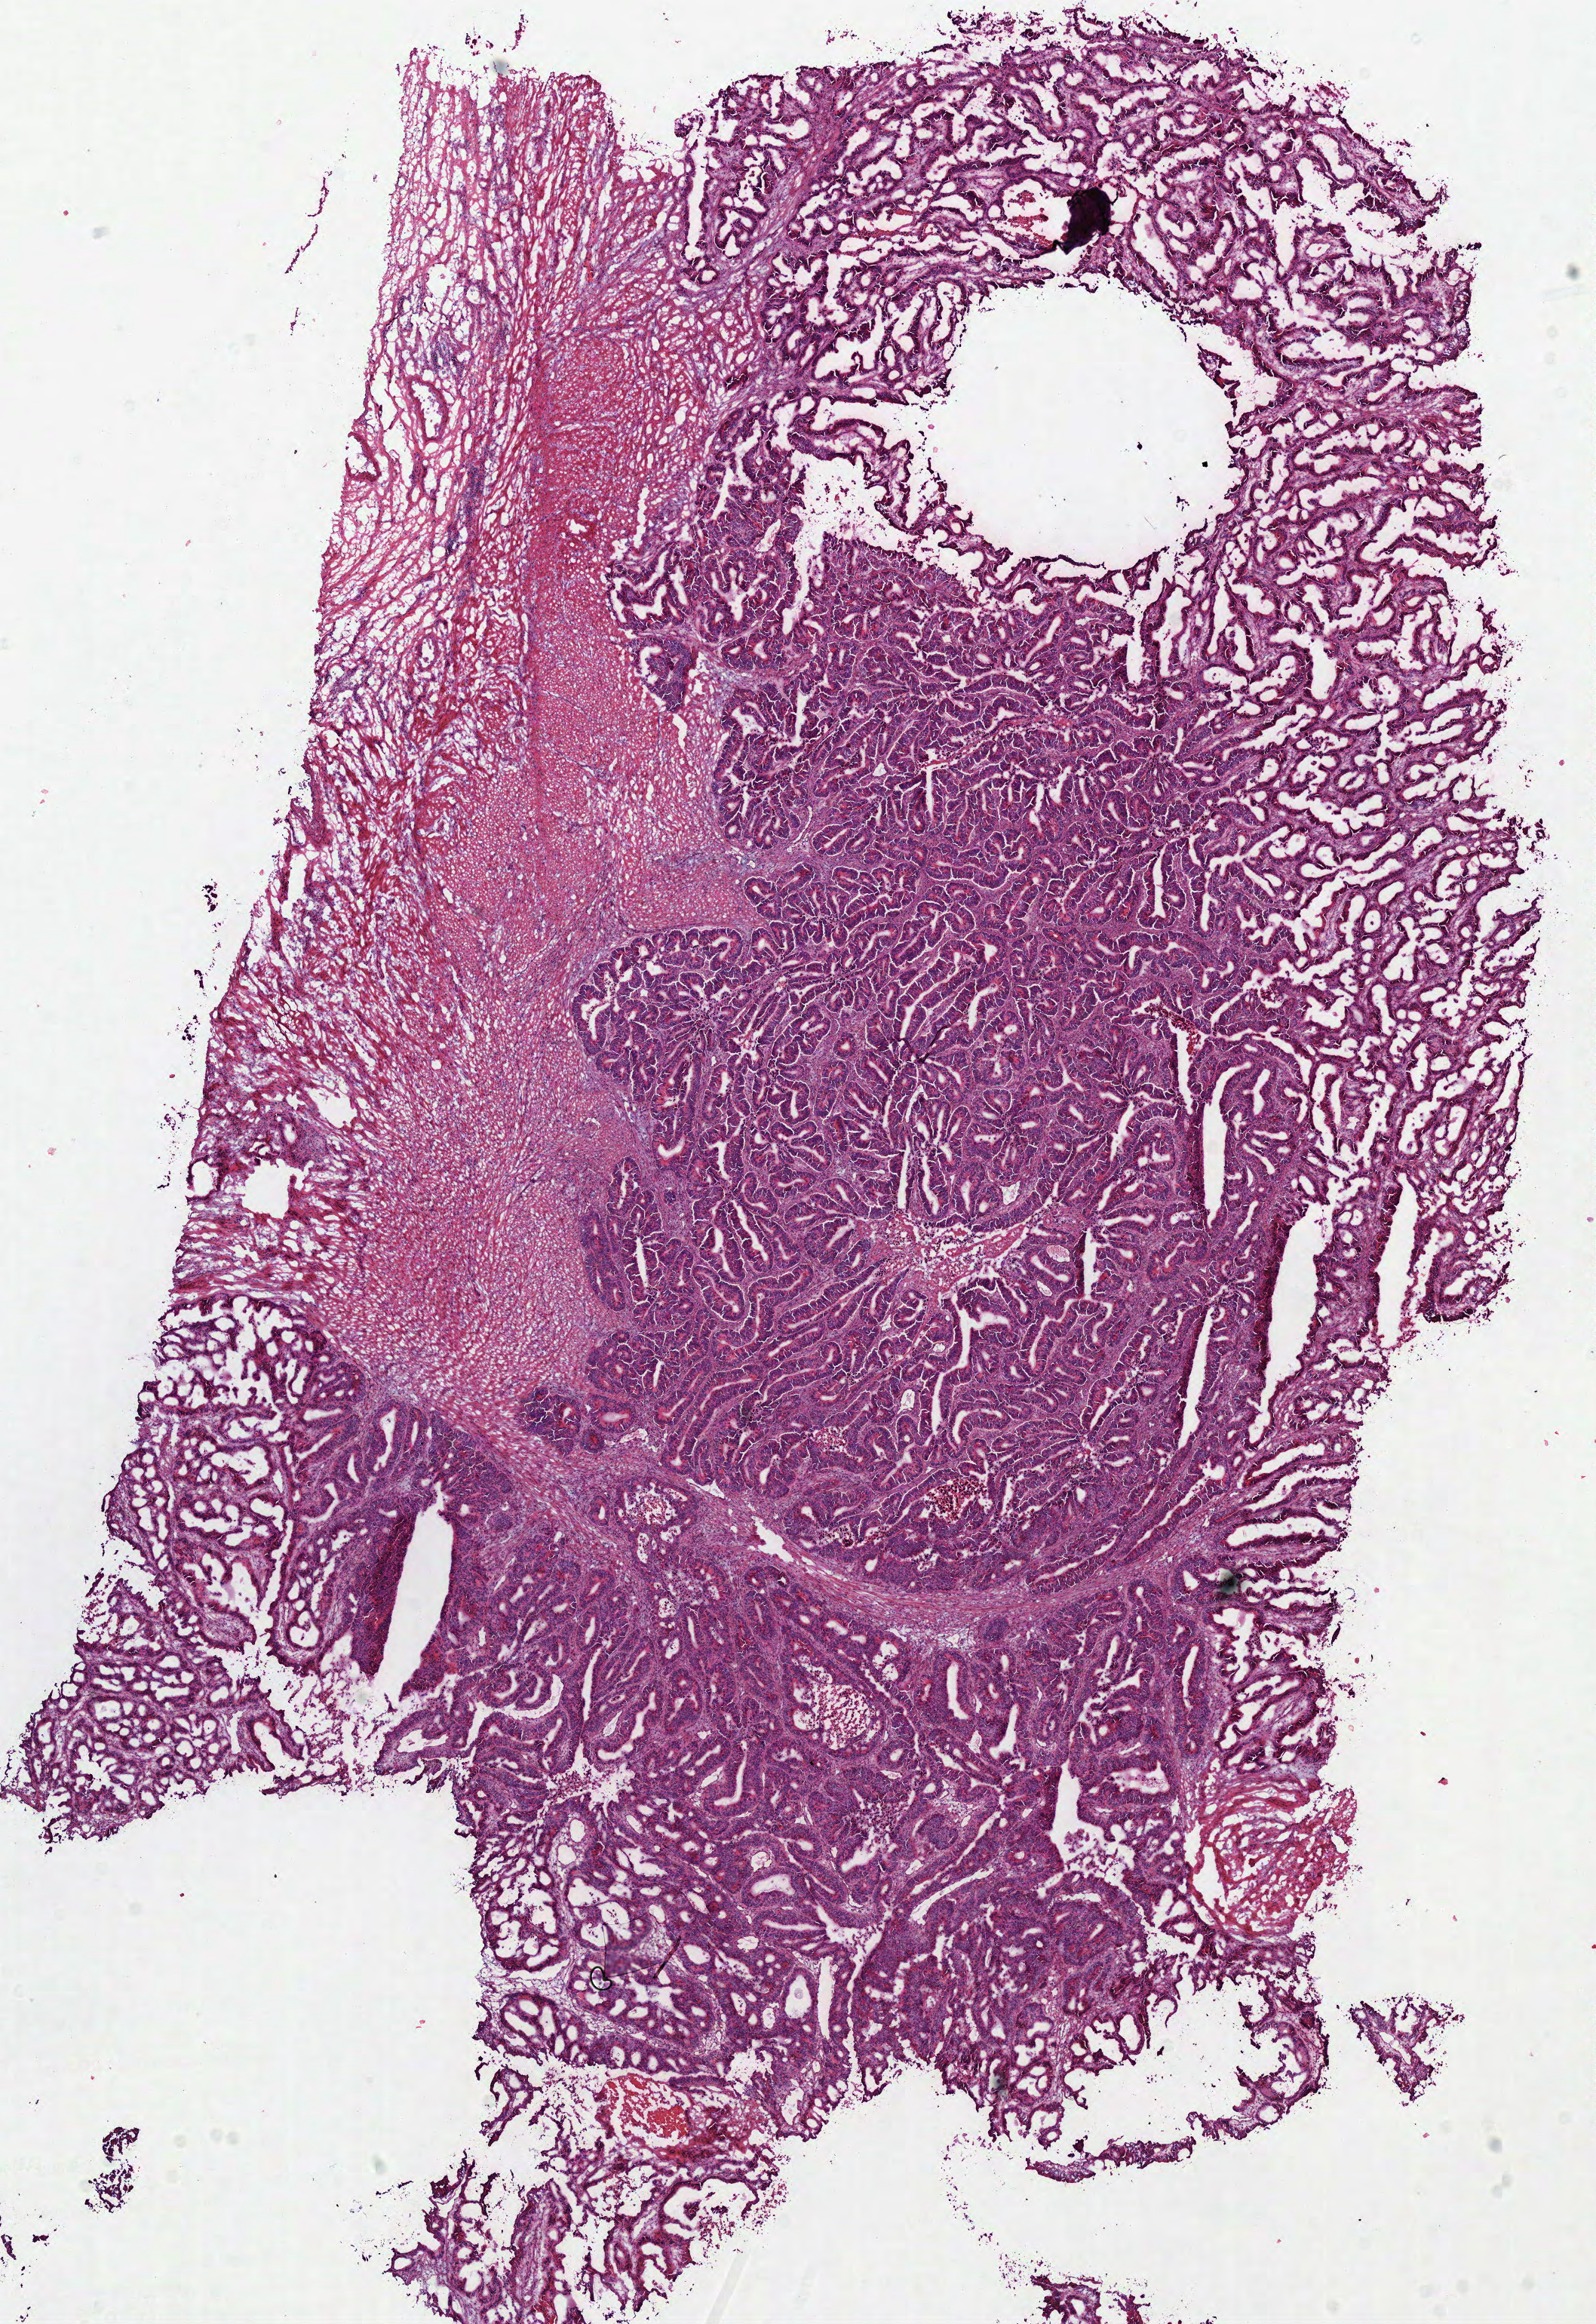
Whole-slide histology image, Hematoxylin and eosin (H&E) stained, low-resolution overview of the scanned area, about 8.3 x 12.1 mm; frozen section from the top of the tissue portion; sample: primary tumour, colon. Patient: male, age at initial diagnosis 65 years. Slide review estimates, as recorded: tumour cells 75%, tumour nuclei 80%, normal cells 0%, stromal cells 20%, necrosis 5%.
TNM: T3 N0 M0. AJCC pathologic stage: IIA. Pathologic diagnosis: Papillary adenocarcinoma, NOS (ascending colon).